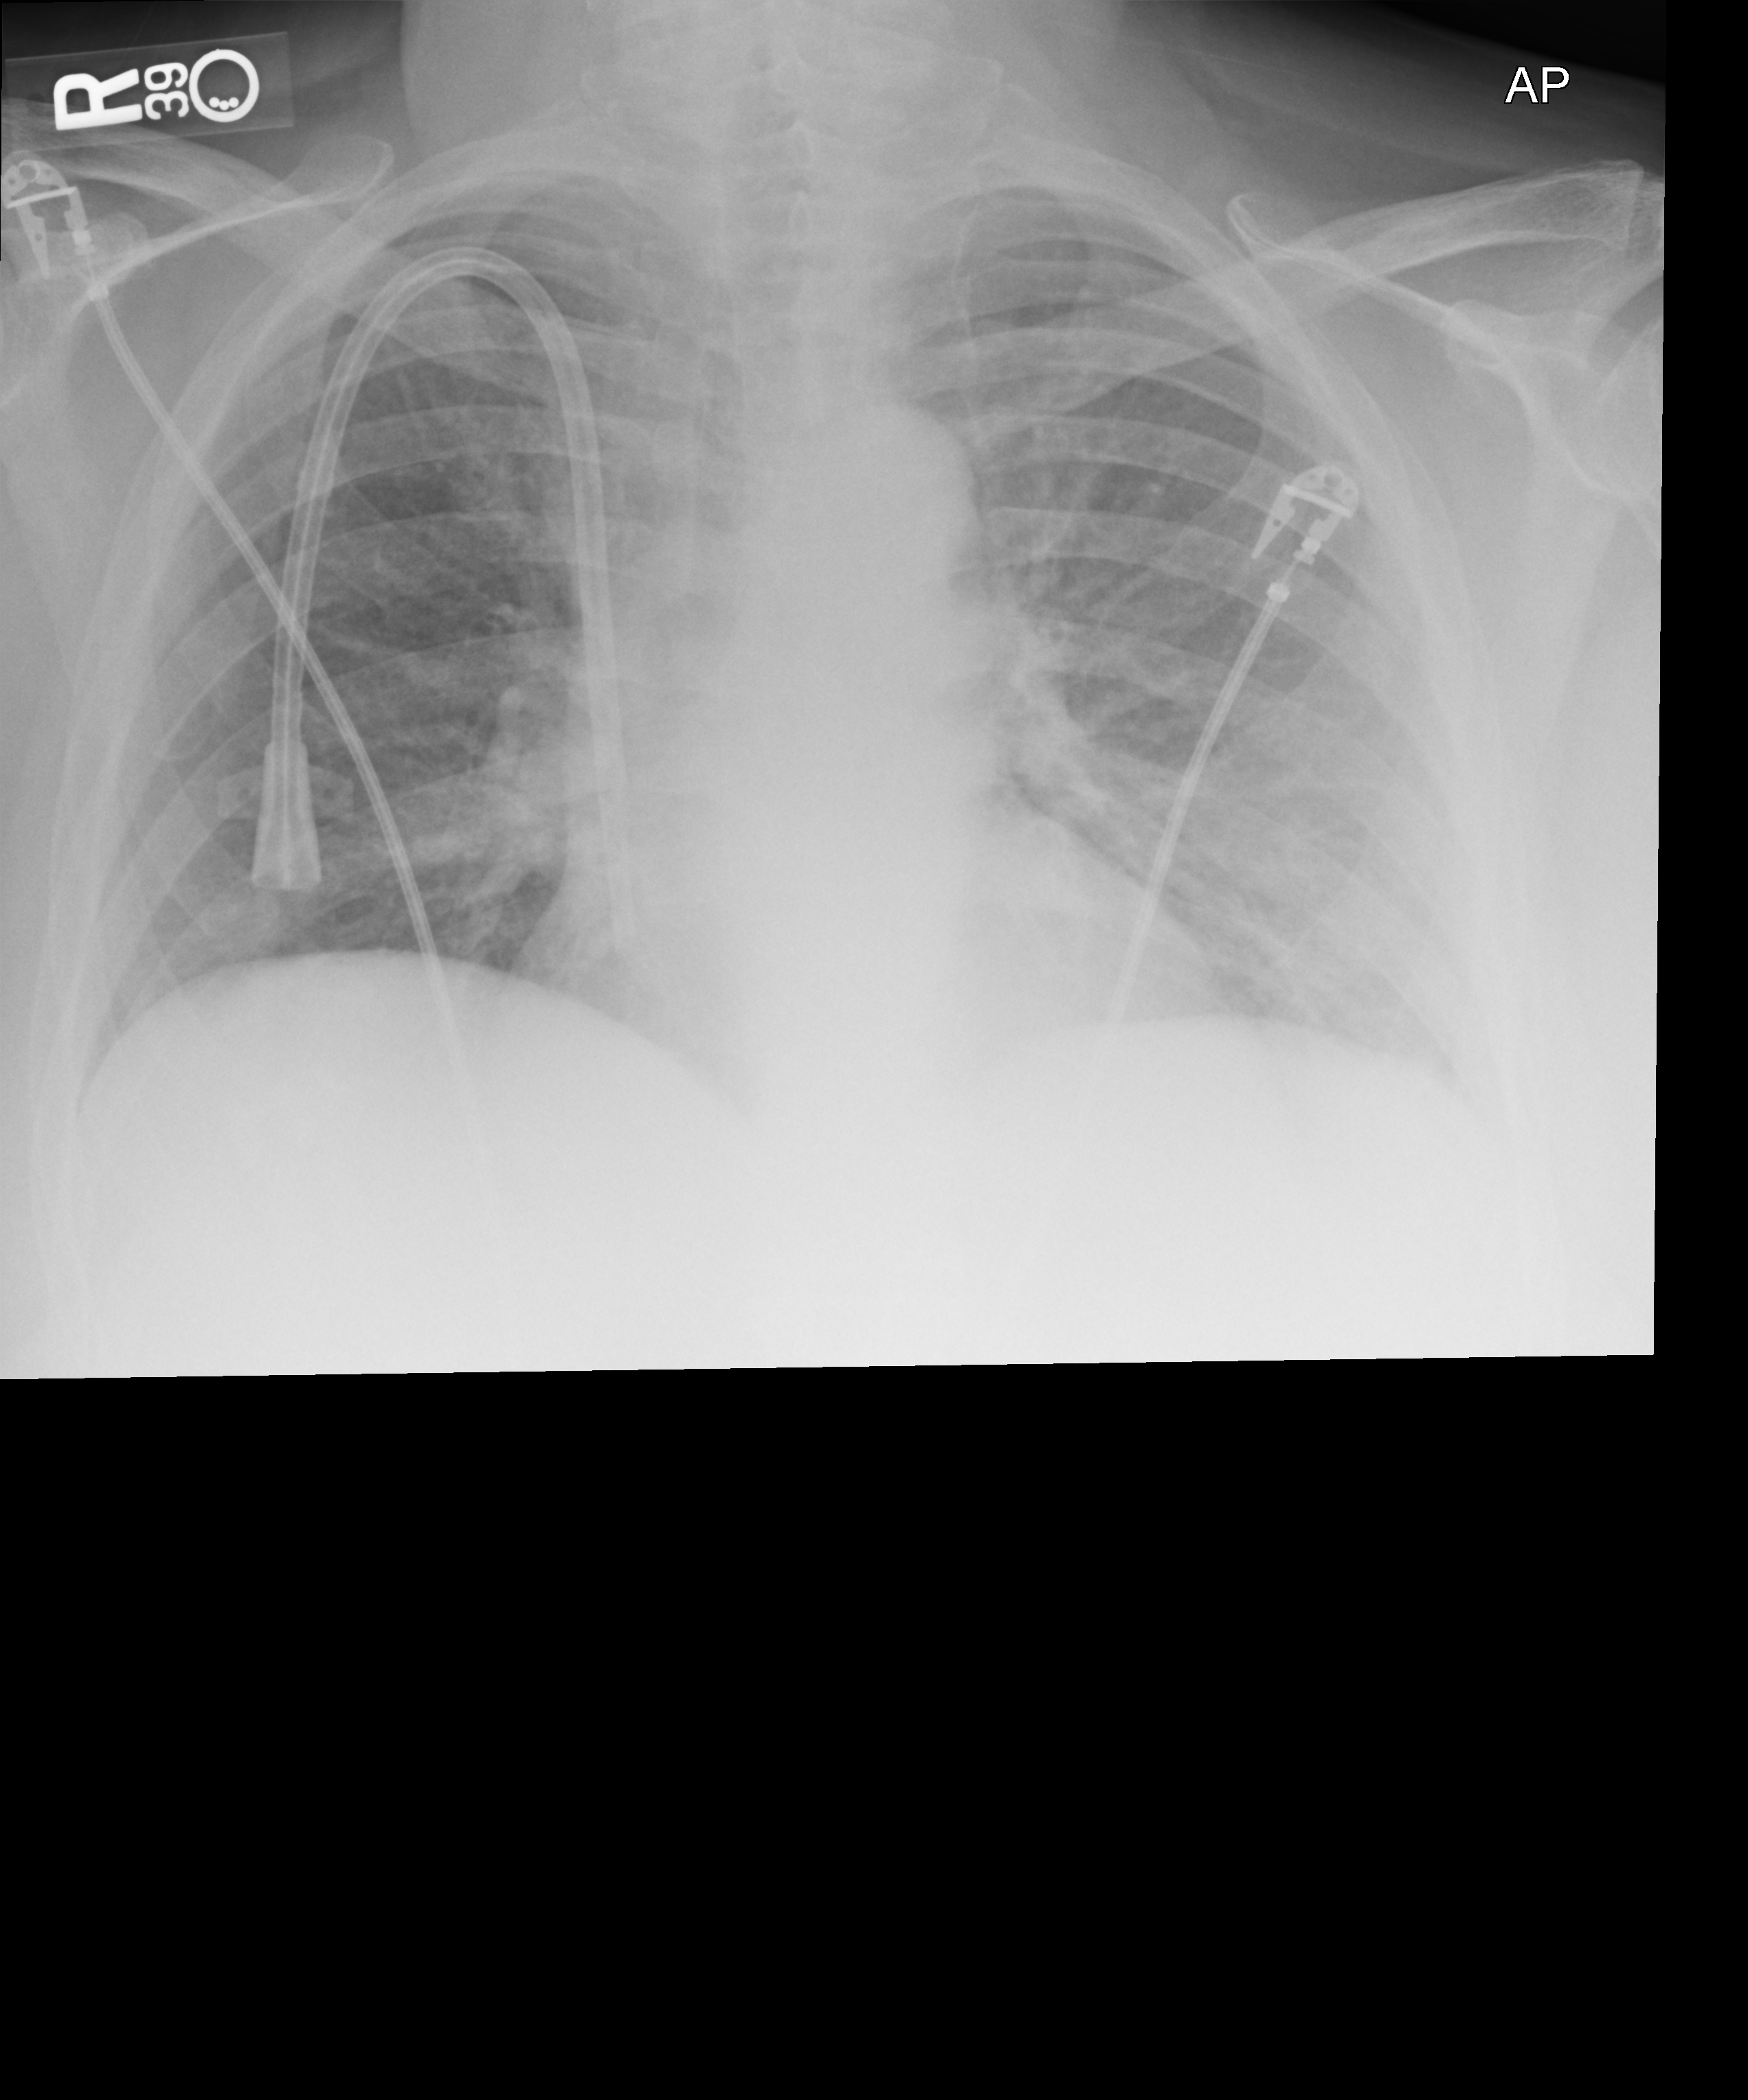
Chest X-ray (portable). Female patient hospitalised with COVID-19, age 60–74 years.
Admission-level facts for this patient (not findings on this image; timing relative to this image not recorded):
- length of hospital stay: 8 days
- mechanically ventilated during this hospital stay: no
- admitted to intensive care during this hospital stay: no